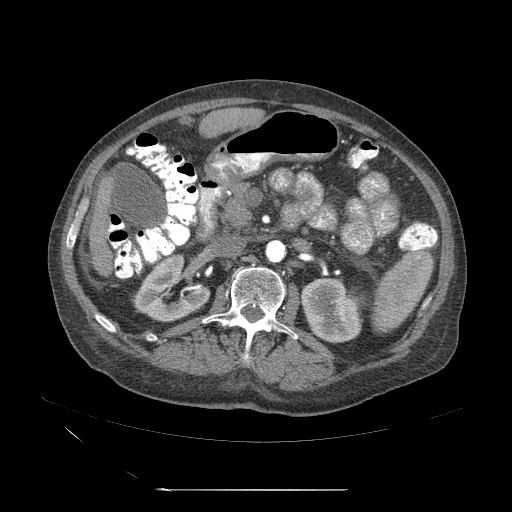
Contrast-enhanced abdominal CT (liver protocol), one axial slice. Slice 13 of 71 in the series (ordered by position). 120 kVp. Soft-tissue window (W 400 / L 40 HU). 2.5 mm slice thickness. 512 × 512 image matrix. Case-level facts recorded for this patient, not image findings: diagnosis: hepatocellular carcinoma (patient treated with transarterial chemoembolisation; whether this scan precedes or follows treatment is not stated here); TNM stage (as recorded): Stage-II; Child-Pugh class: A; tumour nodularity: multinodular.
Outlined on this slice (semi-automatic segmentation, software-assisted and operator-edited):
- abdominal aorta: box from (x=265, y=241) to (x=286, y=264) px